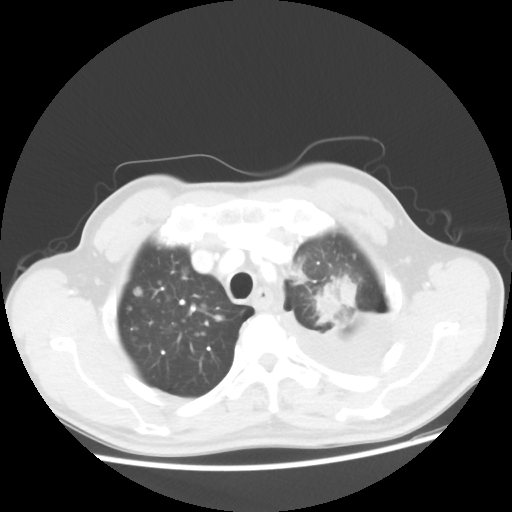
Chest CT, one axial slice. Position 40 of 48 along the scan axis. 100 kVp. Lung window (W 1500 / L -600 HU). 512 × 512 image matrix. Male patient, age 55 years. From the clinical record (not read from this slice): clinical TNM (as recorded): T2 N3 M1a.
Structures marked on this image (rectangle marked by the reading radiologist):
- lung tumour (recorded histology: squamous cell carcinoma): bounding box [x1, y1, x2, y2] px = [304, 277, 374, 334]